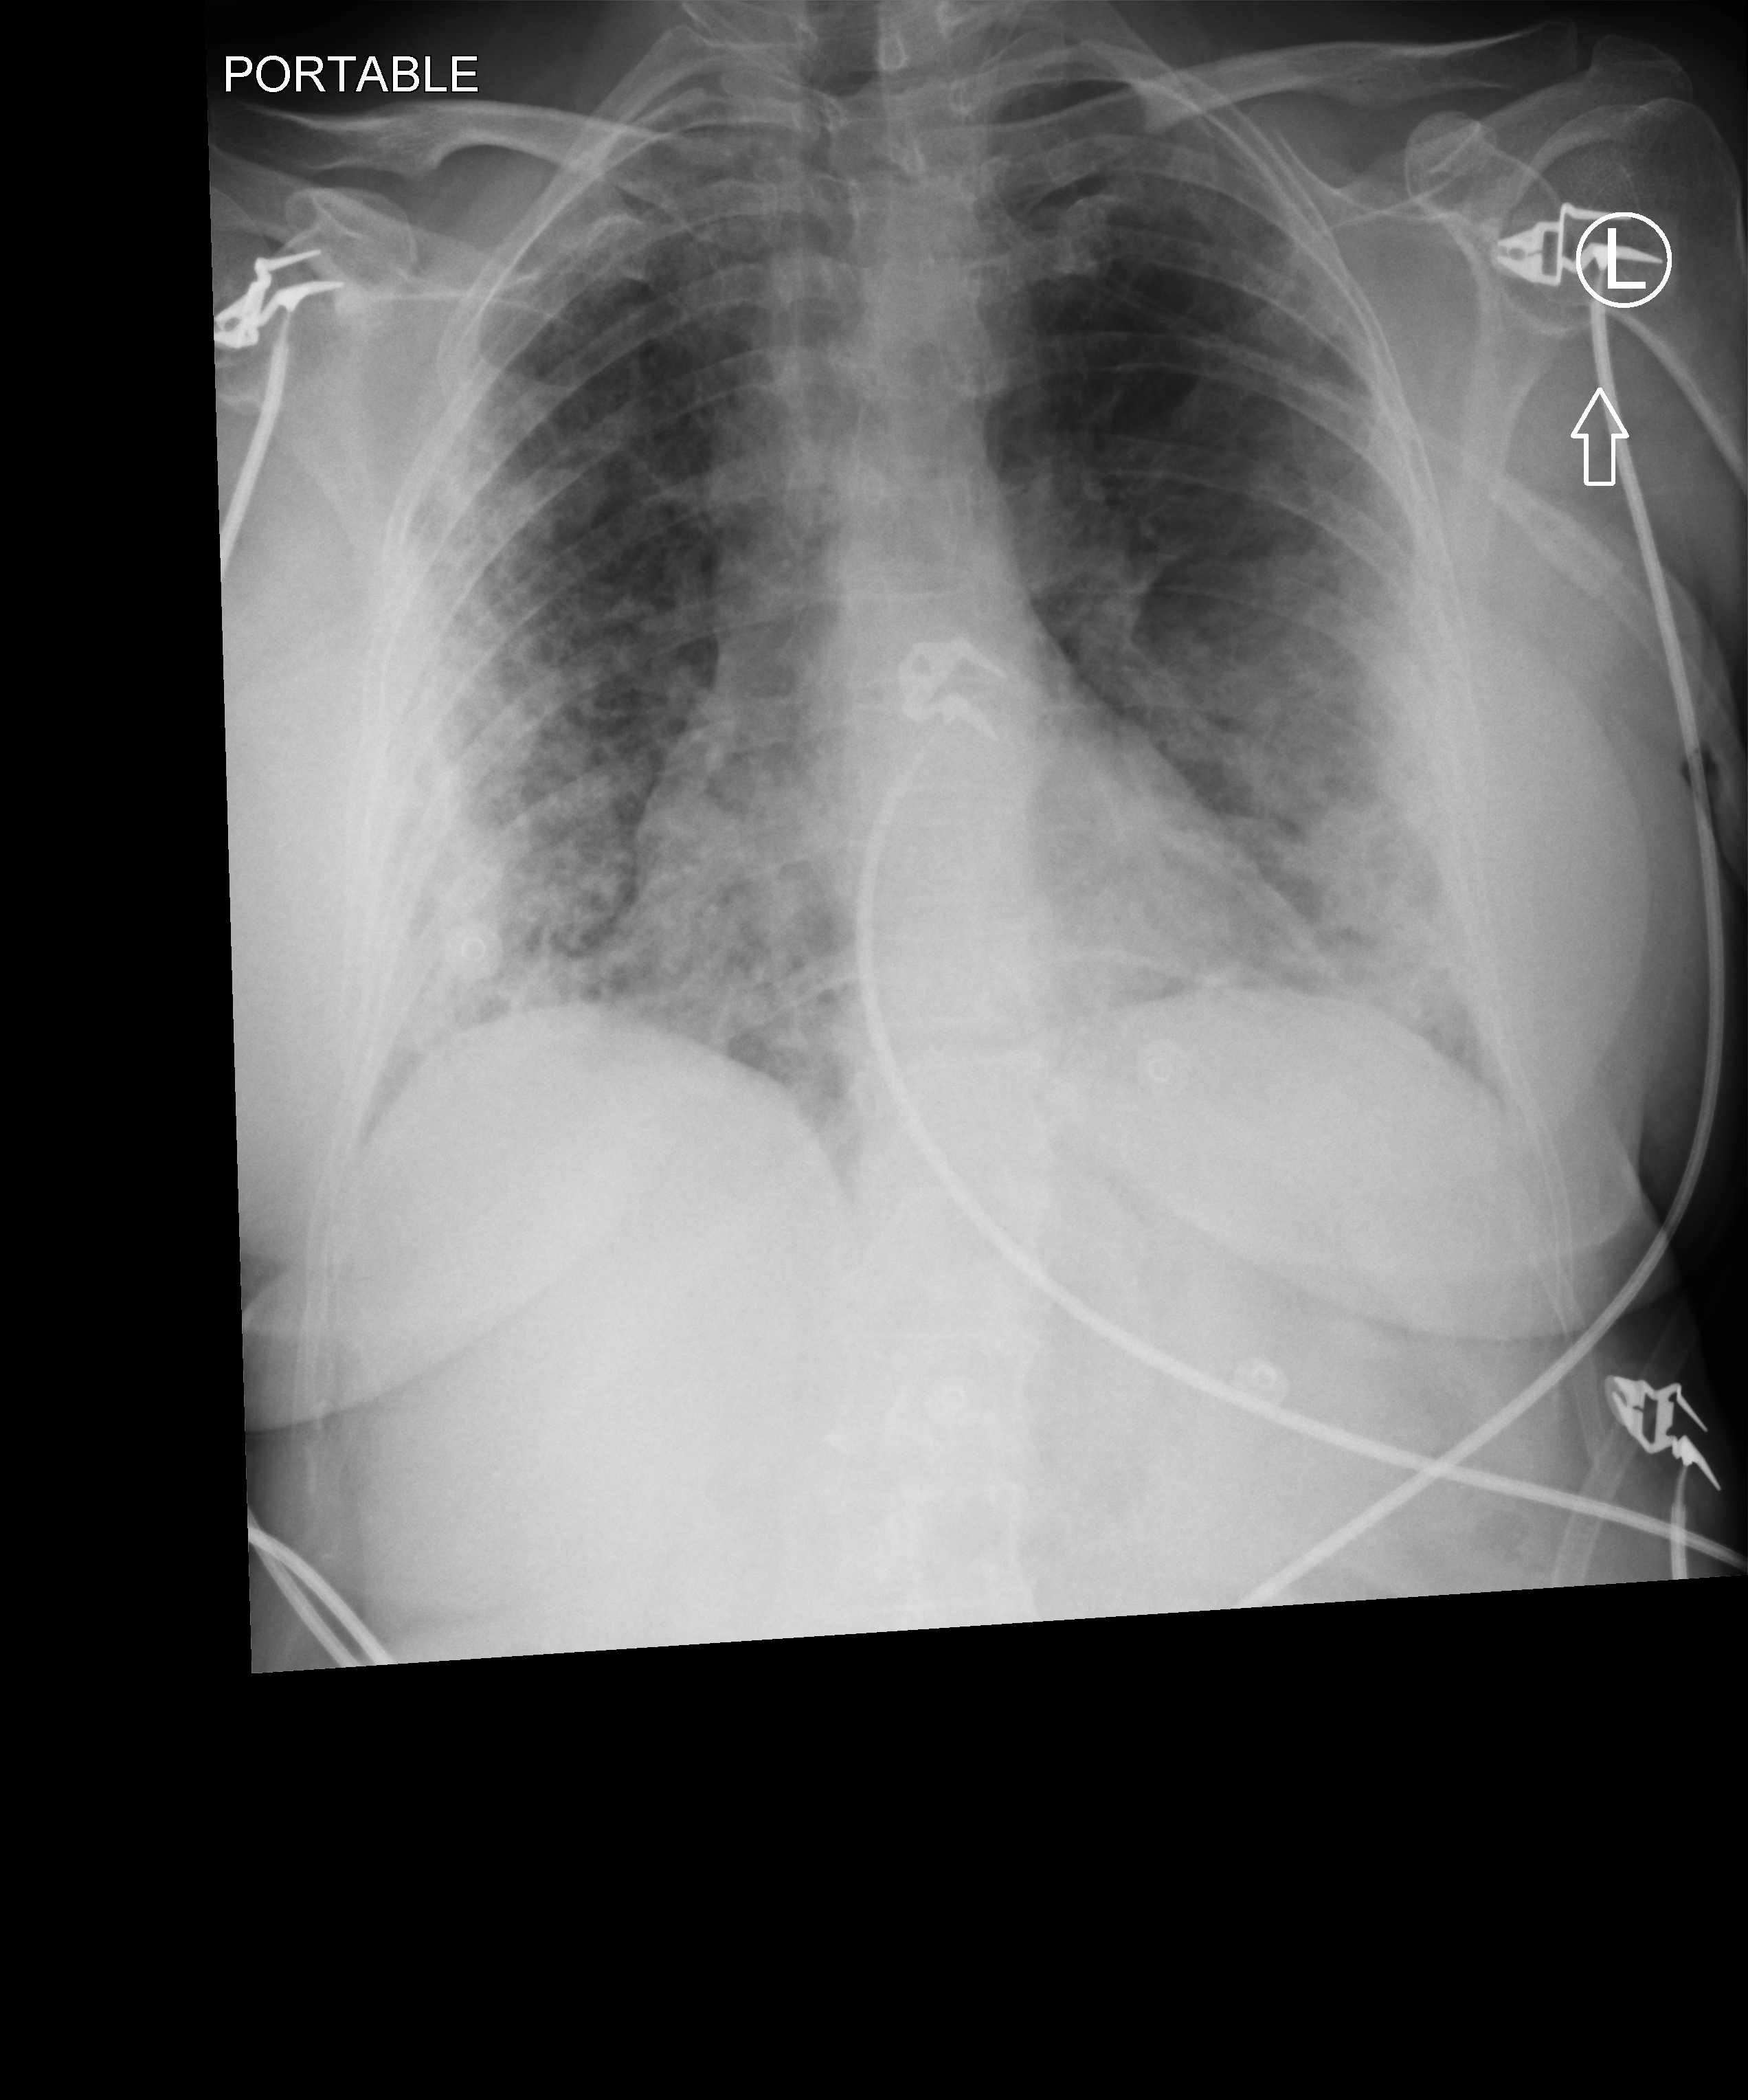
Bedside chest radiograph (computed radiography); anteroposterior (AP) projection. Patient hospitalised with COVID-19; female, aged 60–74 years.
Hospital-stay facts (about this admission, not read from this image; timing relative to this image not recorded):
- length of hospital stay: 11 days
- mechanically ventilated during this hospital stay: no
- smoking status (admission record): former